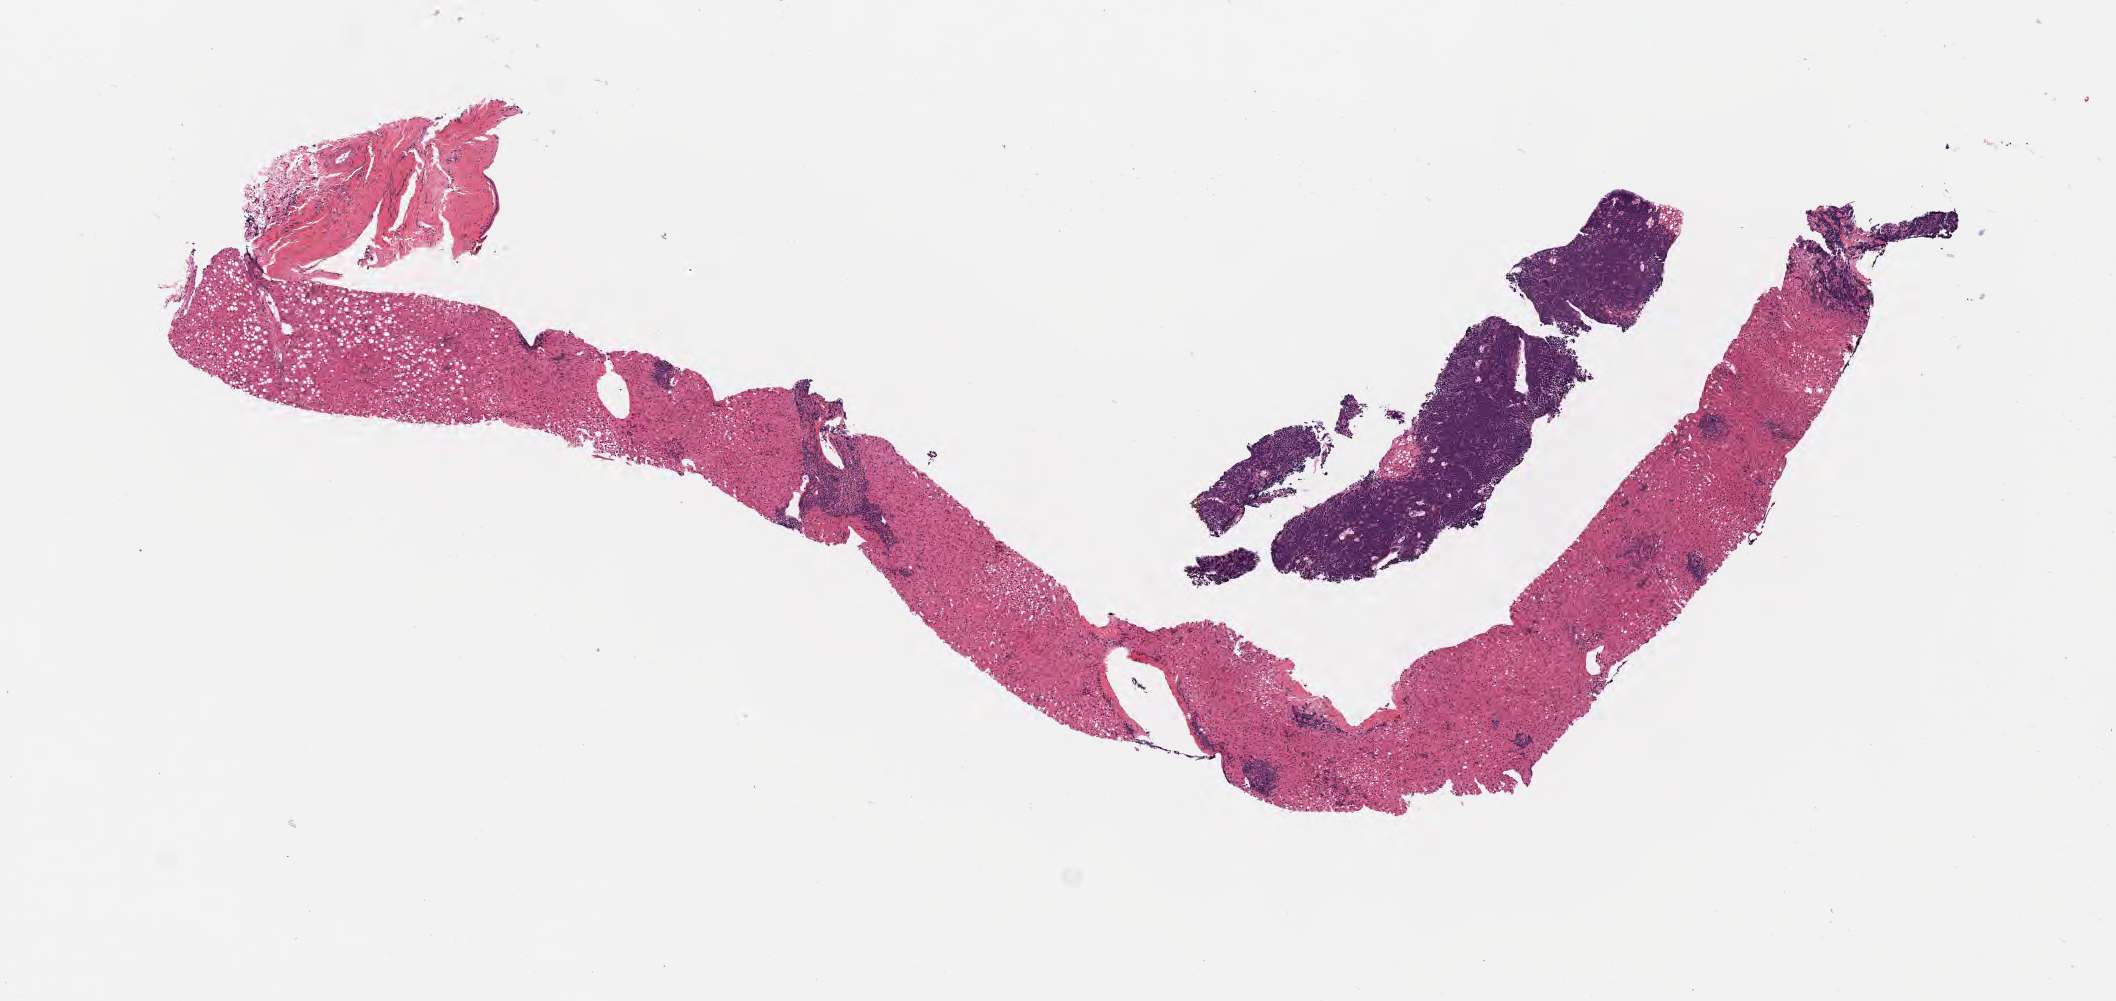
H&E whole-slide image, shown as a low-resolution overview of the whole scanned area (about 8.6 x 4.0 mm). Specimen: tumor tissue. Site: liver. Male, age 7 years at initial diagnosis.
Histologic diagnosis: Burkitt lymphoma, NOS.